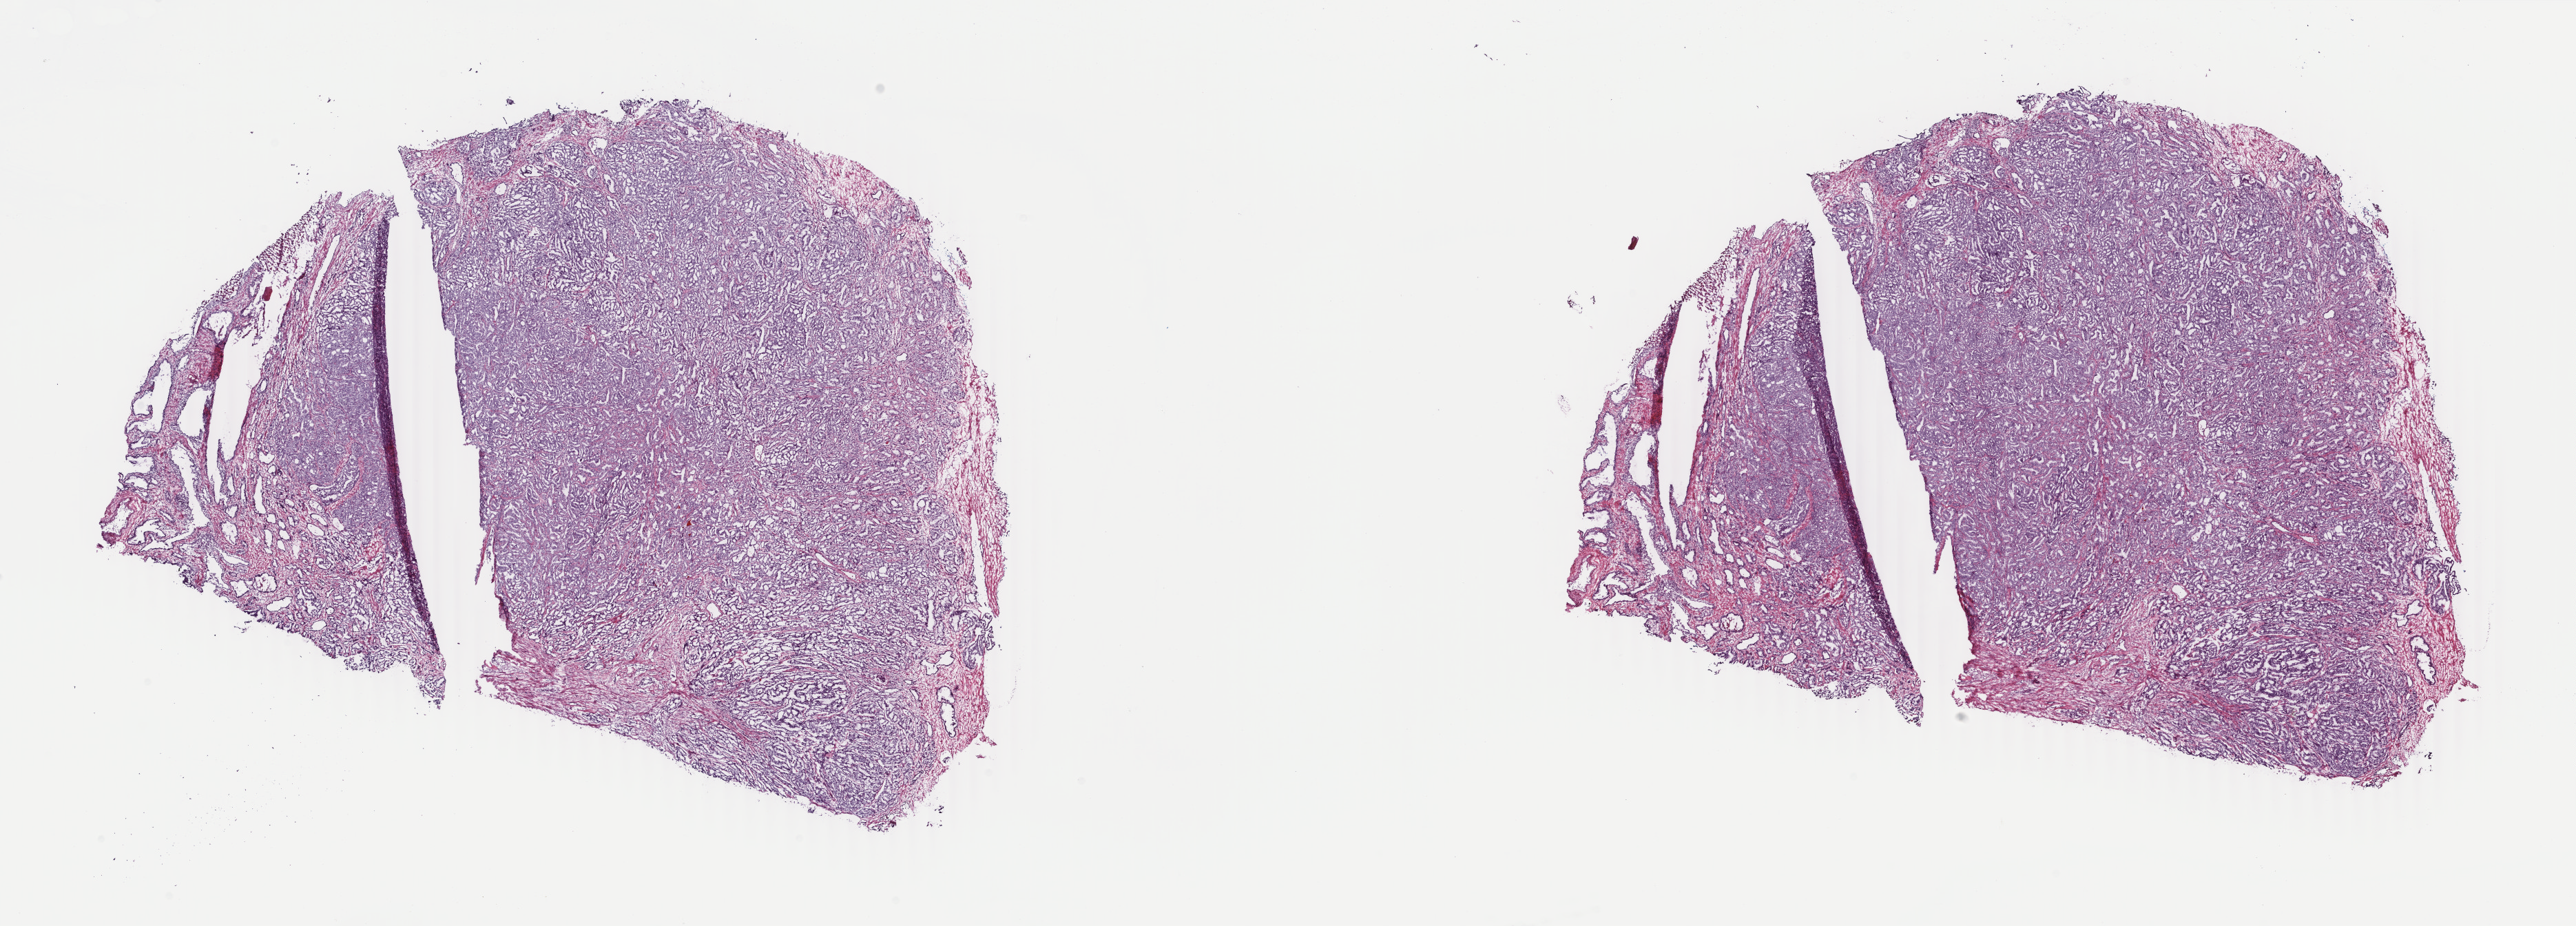
H&E whole-slide image, shown as a low-resolution overview of the whole scanned area (about 29.7 x 10.7 mm, from a 40x scan), frozen section, sample: primary tumour, prostate. Patient: male, age at initial diagnosis 63 years. Gleason score: 8 (4+4). Pathologist review of this section (percent, as recorded): tumour cells 90%, tumour nuclei 95%, normal cells 10%, stromal cells 0%, necrosis 0%. Inflammatory infiltration, as recorded: lymphocyte infiltration 0%, monocyte infiltration 0%, neutrophil infiltration 0%.
* pathologic diagnosis: Adenocarcinoma, NOS
* laterality: right
* lymph nodes positive (case pathology): 0 of 2 examined